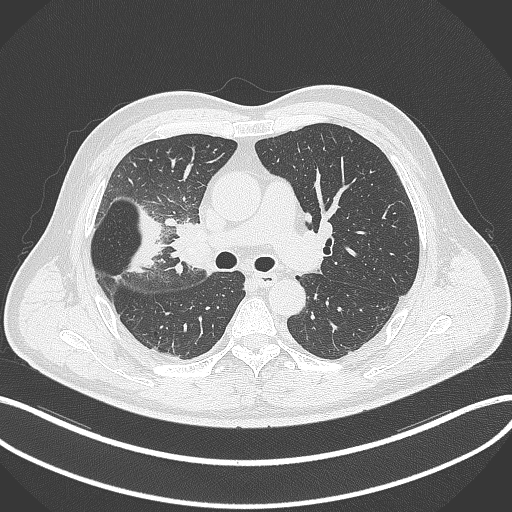
Chest CT, one axial slice; position 201 of 348 along the scan axis; 120 kVp; lung window (W 1500 / L -600 HU); 1 mm slice thickness; 512 × 512 image matrix, field of view 400 × 400 mm. Patient: male, 55 years. From the clinical record (not read from this slice): clinical TNM (as recorded): T3 N2 M1.
Structures marked on this image (rectangle marked by the reading radiologist):
- lung tumour (recorded histology: adenocarcinoma): bounding box <111,197,164,281> (left, top, right, bottom; pixels)